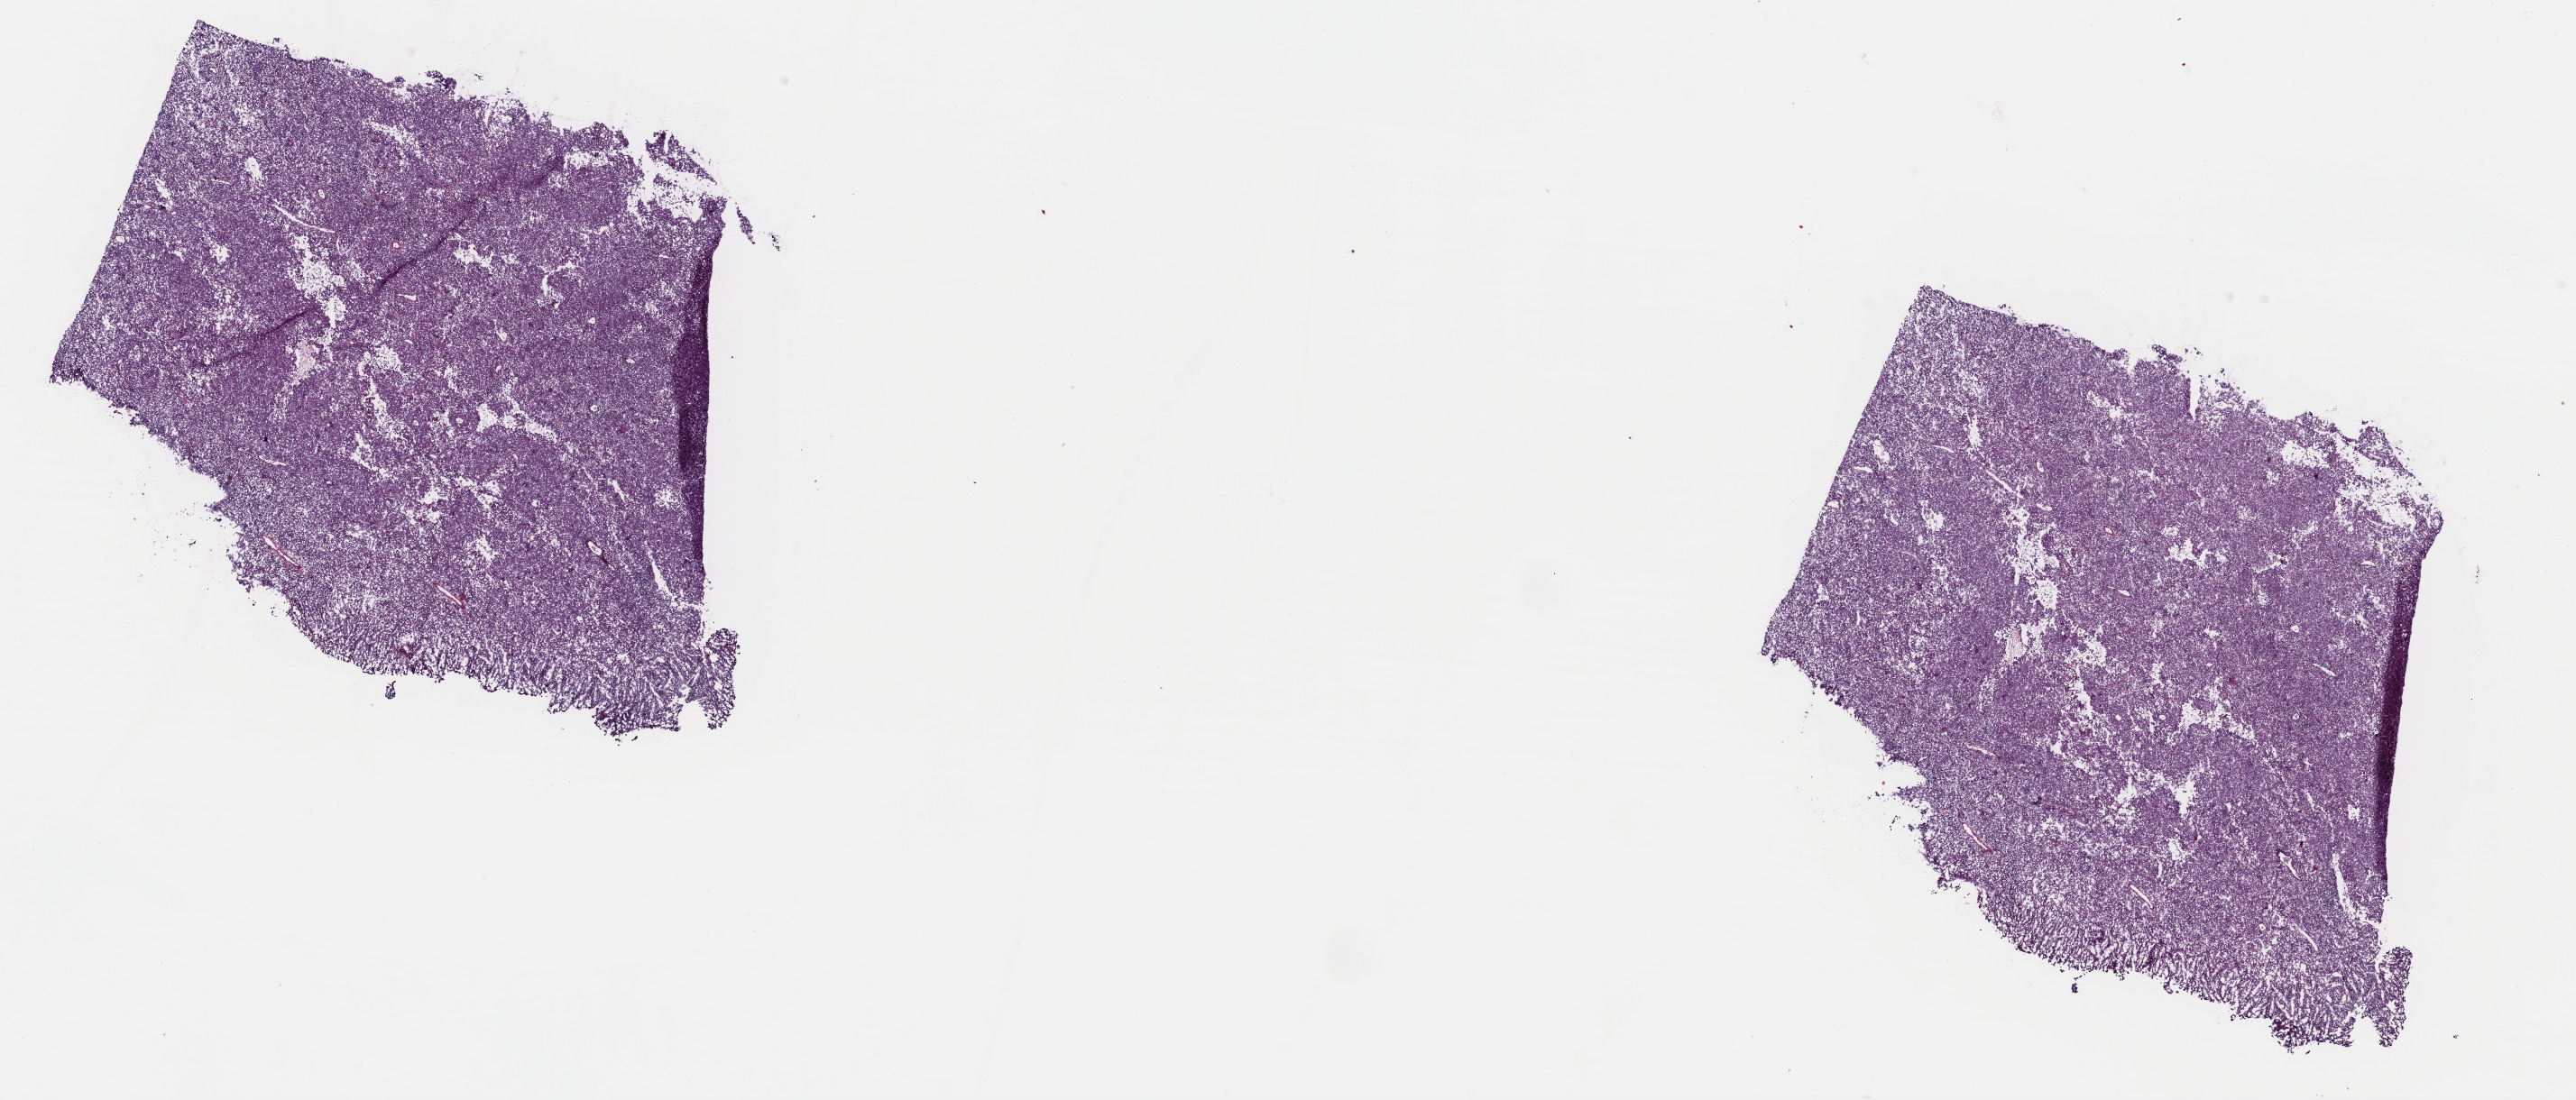
Digitized Hematoxylin and eosin (H&E) stained tissue section (whole slide), low-resolution overview of the scanned area, about 22.6 x 9.6 mm (acquisition: 40x scan), frozen section from the top of the tissue portion, metastatic tumour sample, sampled site: lymph nodes of inguinal region or leg. Patient: female, age at initial diagnosis 51 years. Slide review estimates, as recorded: tumour cells 100%, tumour nuclei 85%, normal cells 0%, stromal cells 0%, necrosis 0%. Infiltration values recorded for this section: lymphocyte infiltration 2%, monocyte infiltration 0%, neutrophil infiltration 0%.
This section: metastatic tumour tissue. Patient diagnosis: Malignant melanoma, NOS.